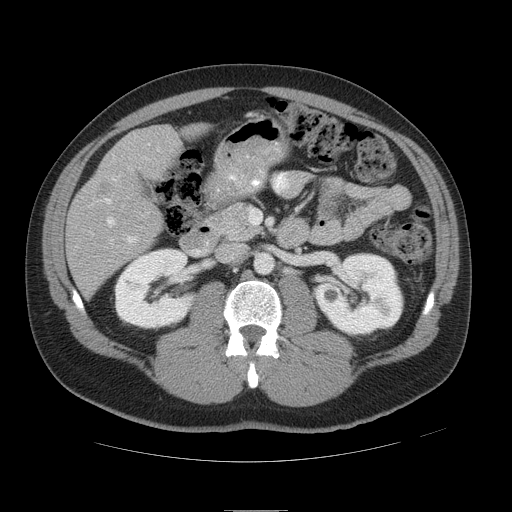
Contrast-enhanced abdominal CT, one axial slice; slice 21 of 49 in the series (ordered by position); 120 kVp; intravenous contrast given; soft-tissue window (W 400 / L 40 HU); 512 × 512 image matrix, field of view 425 × 425 mm. Male patient, age 52 years. Case-level facts recorded for this patient, not image findings: diagnosis: colorectal cancer liver metastases, imaged before liver resection; multiple liver metastases: yes; largest metastasis: 5.1 cm; disease in both lobes: yes.
Outlined on this slice (outlined manually by an expert reader):
- hepatic veins: box from (x=107, y=143) to (x=151, y=226) px
- liver: (x=68, y=126)–(x=181, y=293)
- planned liver remnant (the part of the liver to remain after resection): (x=133, y=126)–(x=181, y=166)
- portal vein (with intrahepatic branches): (x=96, y=175)–(x=138, y=244)
- liver metastasis: (x=97, y=183)–(x=112, y=197)